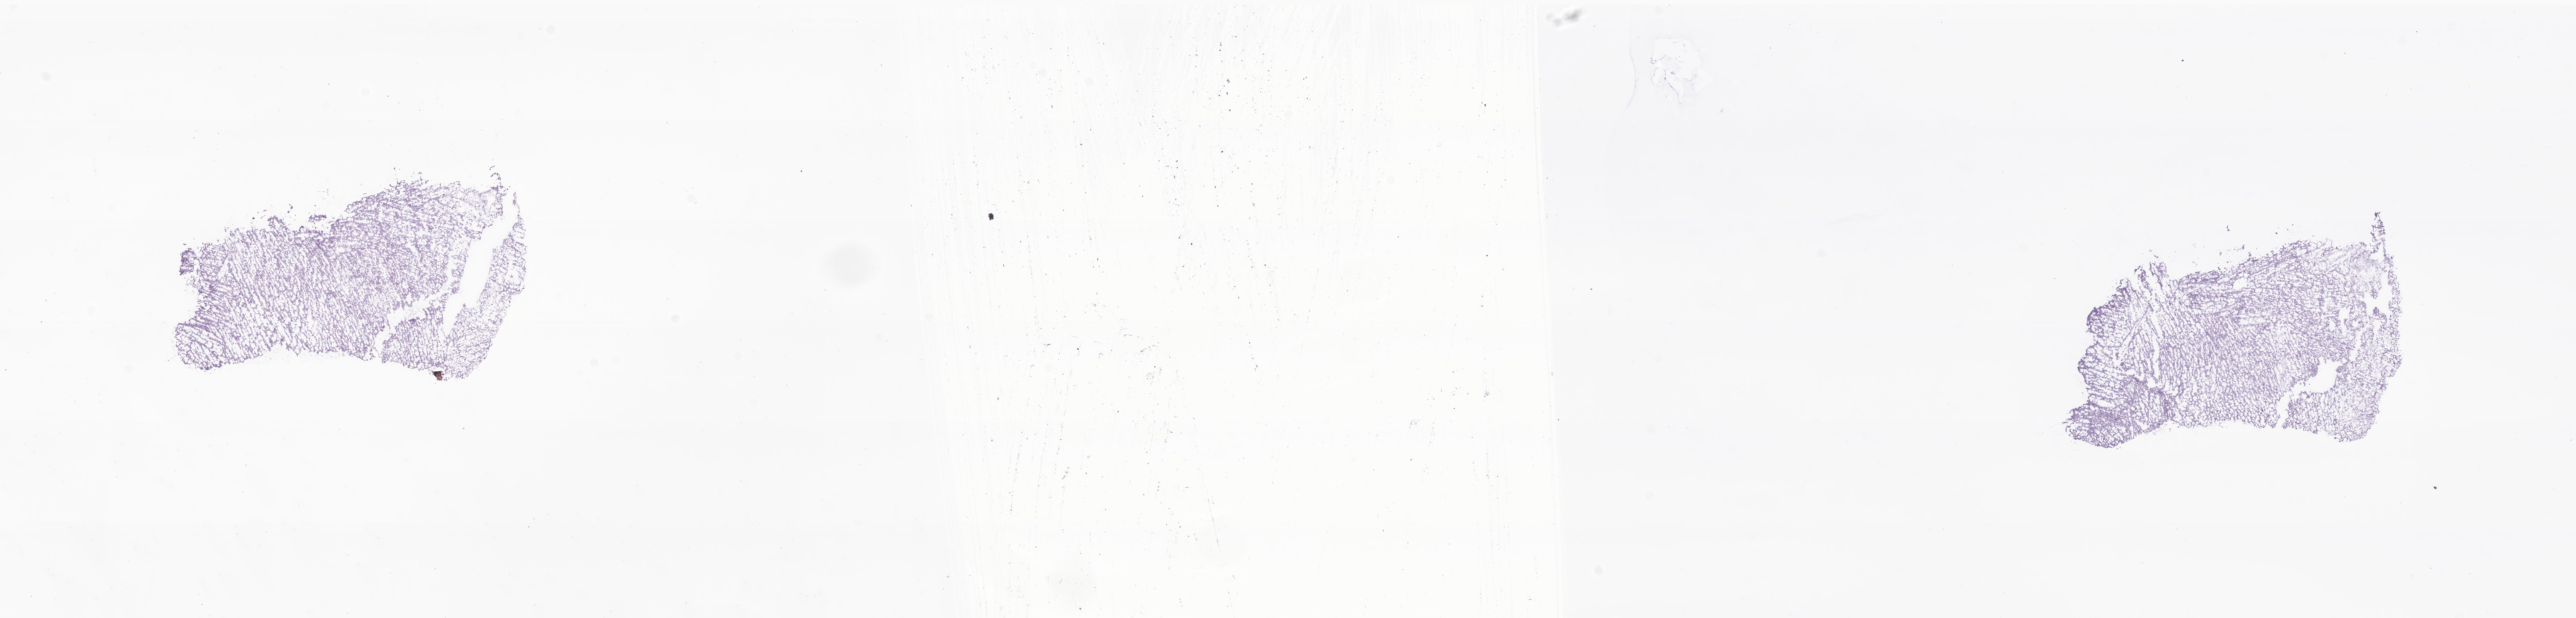
Digitized H&E-stained section of tumor tissue from the testis, low-resolution overview of the scanned area, about 27.3 x 6.6 mm. Frozen section. Male patient, age 982 days (about 2.7 years).
Recorded diagnosis: Embryonal rhabdomyosarcoma, NOS.